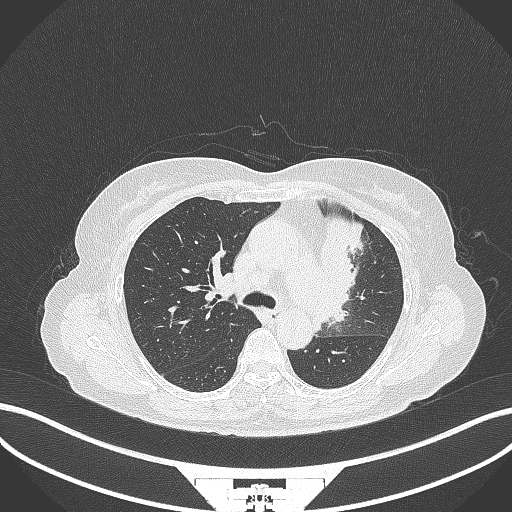
Chest CT, one axial slice; position 220 of 382 along the scan axis; reconstruction kernel B70f; lung window (W 1500 / L -600 HU); 1 mm slice thickness; 512 × 512 image matrix. Patient: female, 64 years. From the clinical record (not read from this slice): clinical TNM (as recorded): T2a N2 M0.
Outlined on this slice (bounding box drawn by a radiologist):
- lung tumour (recorded histology: adenocarcinoma): box from (x=309, y=210) to (x=367, y=336) px